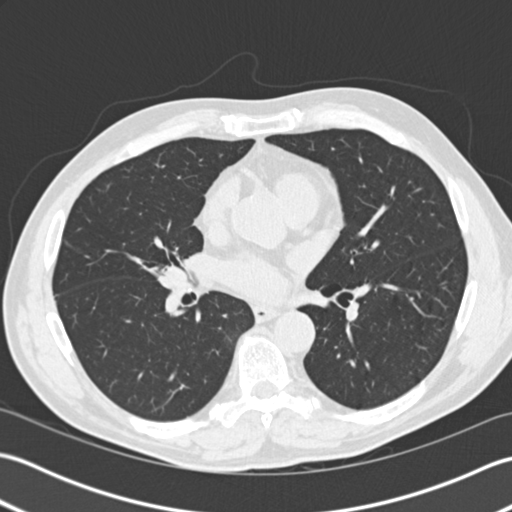
Low-dose screening chest CT, axial slice; second annual screen; lung window (W 1500 / L -600 HU); standard (soft-tissue) reconstruction kernel (B30f); 140 kVp; slice 99 of 192 in the series. Male participant, aged 57 years at enrolment. Former smoker at enrolment.
Expert-annotated lung lesion, box from (x=156, y=253) to (x=196, y=291) px. No non-calcified nodule or mass ≥4 mm was recorded by the screening reader at this exam. Official screen result: negative screen, significant abnormalities not suspicious for lung cancer. Later outcome: lung cancer diagnosed 483 days after this screen — carcinoid tumor, NOS, right middle lobe, carcinoid, stage not assessed, 15 mm at pathology.